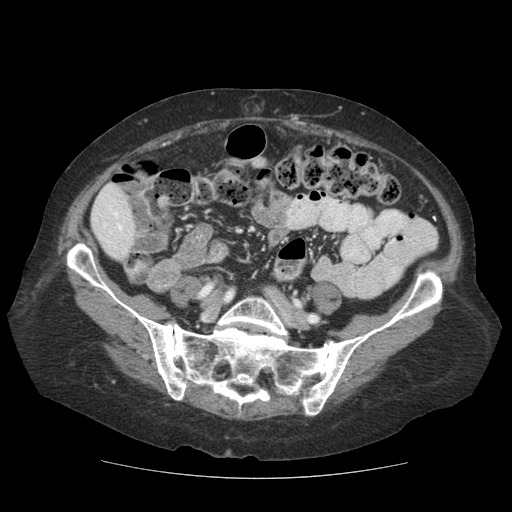
Contrast-enhanced abdominal CT (liver protocol), one axial slice. Slice 17 of 111 in the series (ordered by position). Reconstruction kernel STANDARD. 140 kVp. Soft-tissue window (W 400 / L 40 HU). 2.5 mm slice thickness. 512 × 512 image matrix. Case-level facts recorded for this patient, not image findings: diagnosis: hepatocellular carcinoma (patient treated with transarterial chemoembolisation; whether this scan precedes or follows treatment is not stated here); TNM stage (as recorded): Stage-I; Child-Pugh class: A; tumour differentiation: moderately-poorly differentiated; tumour nodularity: uninodular.
Outlined on this slice (semi-automatic segmentation, software-assisted and operator-edited):
- liver parenchyma outside the tumour (the mass and vessels are separate outlines, so this box may not span the whole liver): bounding box [x1, y1, x2, y2] px = [90, 184, 136, 260]
- liver vessels: [113, 211, 122, 230]